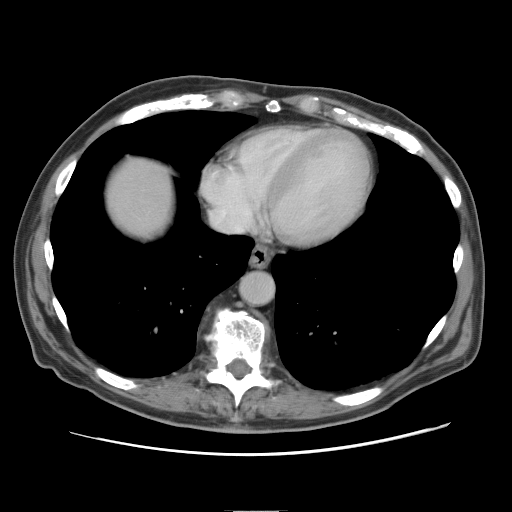
Contrast-enhanced abdominal CT, one axial slice; slice 79 of 89 in the series (ordered by position); 120 kVp; intravenous contrast given; soft-tissue window (W 400 / L 40 HU); 512 × 512 image matrix, field of view 375 × 375 mm. Male patient, age 69 years. Case-level facts recorded for this patient, not image findings: diagnosis: colorectal cancer liver metastases, imaged before liver resection; multiple liver metastases: no; largest metastasis: 8.5 cm.
Outlined on this slice (manually delineated by an expert):
- liver: bounding box (x1, y1, x2, y2) in pixels: (105, 158, 173, 238)
- planned liver remnant (the part of the liver to remain after resection): (105, 158, 174, 238)